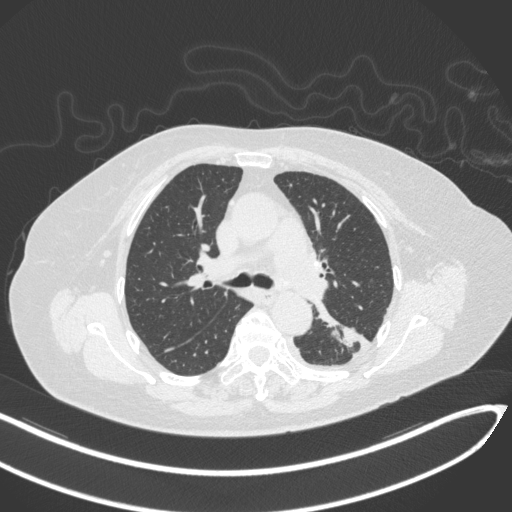
Chest CT, one axial slice. Position 203 of 270 along the scan axis. Reconstruction kernel B31f. 120 kVp. Lung window (W 1500 / L -600 HU). 512 × 512 image matrix, field of view 400 × 400 mm. Female patient, age 76 years. From the clinical record (not read from this slice): clinical TNM (as recorded): T1c N0 M0.
Annotated regions visible in this slice (rectangle marked by the reading radiologist):
- lung tumour (recorded histology: adenocarcinoma): bounding box <312,296,360,346> (left, top, right, bottom; pixels)